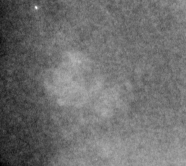
Cropped region of a digitized screen-film mammogram centred on a radiologist-marked abnormality; left breast; CC view; BI-RADS breast density category 4 (scale 1–4).
Marked abnormality: calcifications, morphology amorphous, distribution clustered; BI-RADS assessment category 4; pathology result (as recorded, not read from the image): malignant.